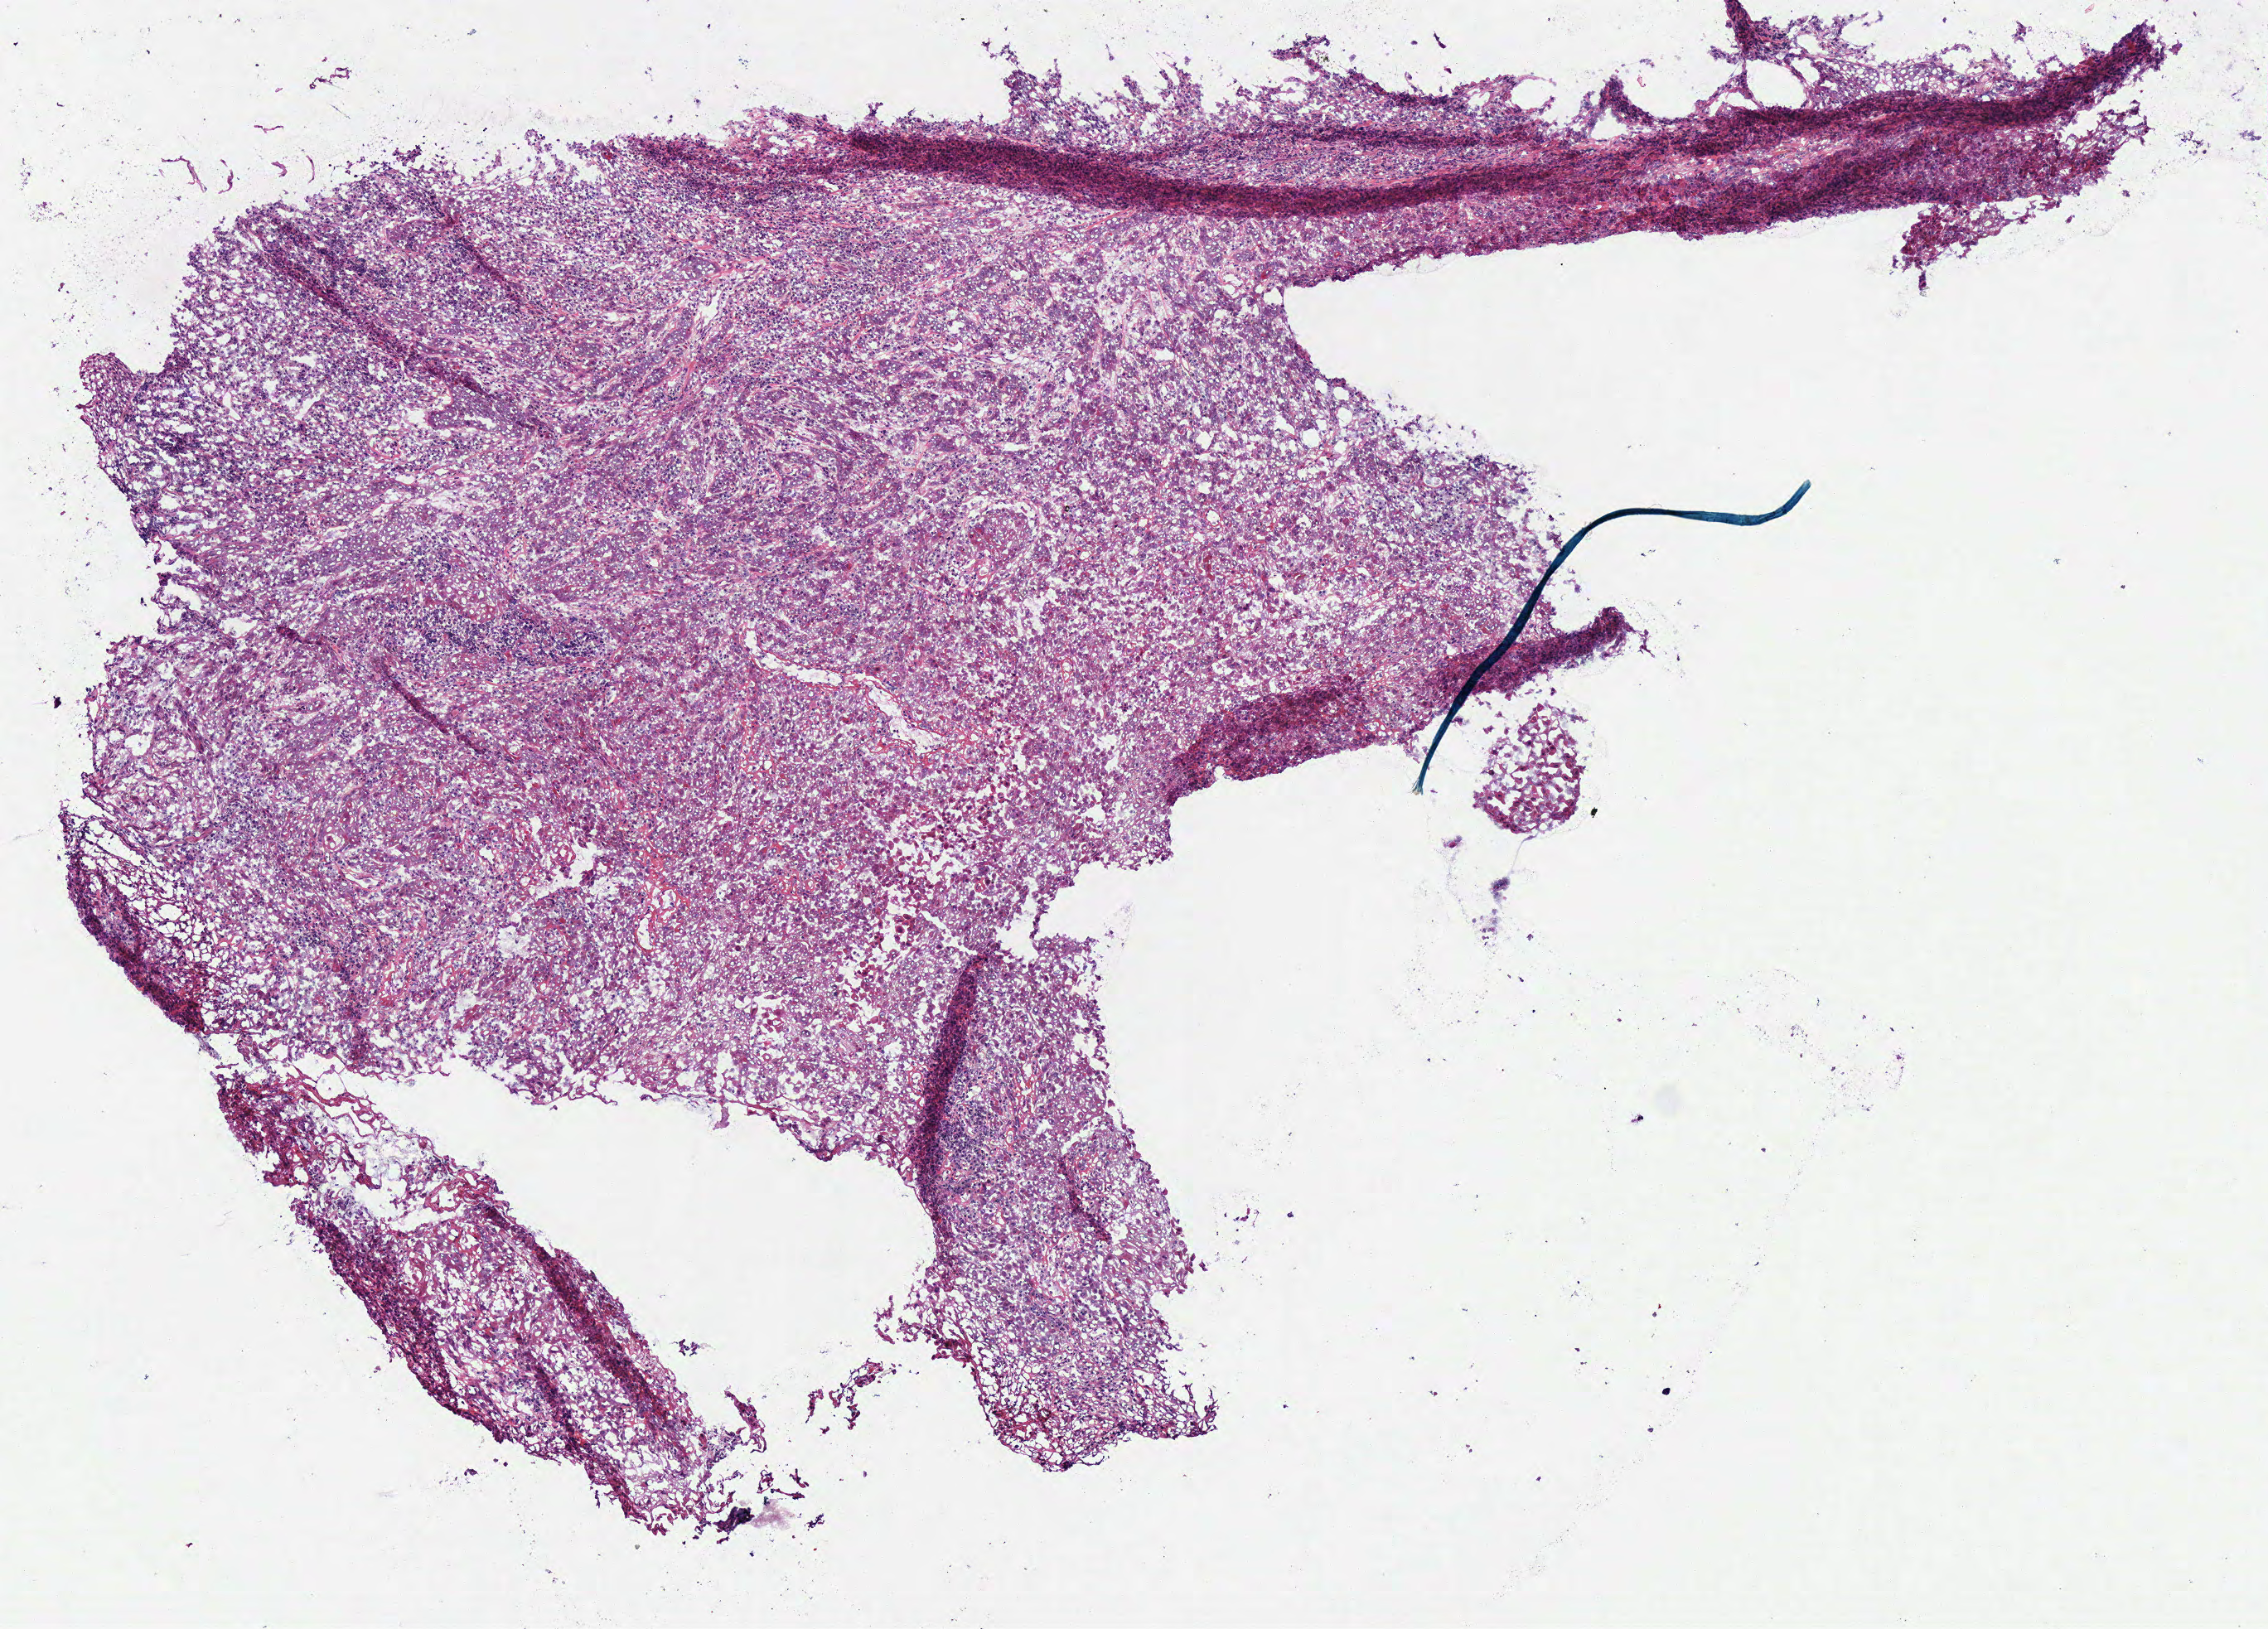
Whole-slide histology image, H&E-stained, low-resolution overview of the scanned area, about 5.4 x 3.9 mm (from a 40x scan). Frozen section from the top of the tissue portion. Primary tumour sample from the head and neck. Patient: female, age at initial diagnosis 60 years. Histologic grade: G2 (moderately differentiated). Pathologist review of this section (percent, as recorded): tumour cells 97%, tumour nuclei 98%, normal cells 0%, stromal cells 2%, necrosis 1%. Inflammatory infiltration, as recorded: neutrophil infiltration 1%.
* histologic diagnosis: Squamous cell carcinoma, NOS
* laterality: left